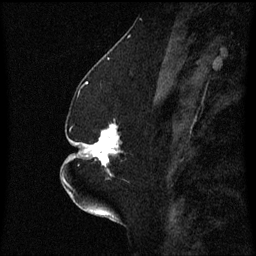
Breast MRI (dynamic contrast-enhanced), one sagittal slice; position 24 of 60 along the scan axis; dynamic contrast-enhanced series, image 2 of 3 at this slice position (ordered by acquisition); 1.5 T; TE 4.2 ms, TR 8.4 ms; 2.3 mm slice thickness; 256 × 256 image matrix, field of view 200 × 200 mm. Patient: female, 52 years. From the clinical record (not read from this slice): setting: breast cancer imaged before/during neoadjuvant chemotherapy; receptor status: HR-positive, HER2-negative.
Outlined on this slice (semi-automatically segmented with operator editing):
- analysis volume of interest (the breast-tissue region the enhancement analysis was run in; not a lesion): bounding box (x1, y1, x2, y2) in pixels: (75, 120, 126, 181)
- tumour enhancement mask (voxels above the 70 % enhancement threshold inside the analysis volume of interest): (75, 124, 119, 171)